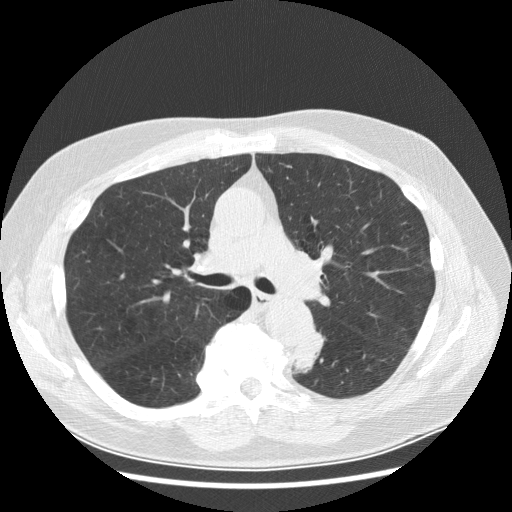
Low-dose screening chest CT, one axial slice; slice 179 of 282 in the series (ordered by position); reconstruction kernel STANDARD; 120 kVp; lung window (W 1500 / L -600 HU); 2.5 mm slice thickness; 512 × 512 image matrix, field of view 370 × 370 mm.
Structures marked on this image (expert manual segmentation):
- lesion 1 (tumor, lower lobe of left lung): bounding box <293,330,325,373> (left, top, right, bottom; pixels)